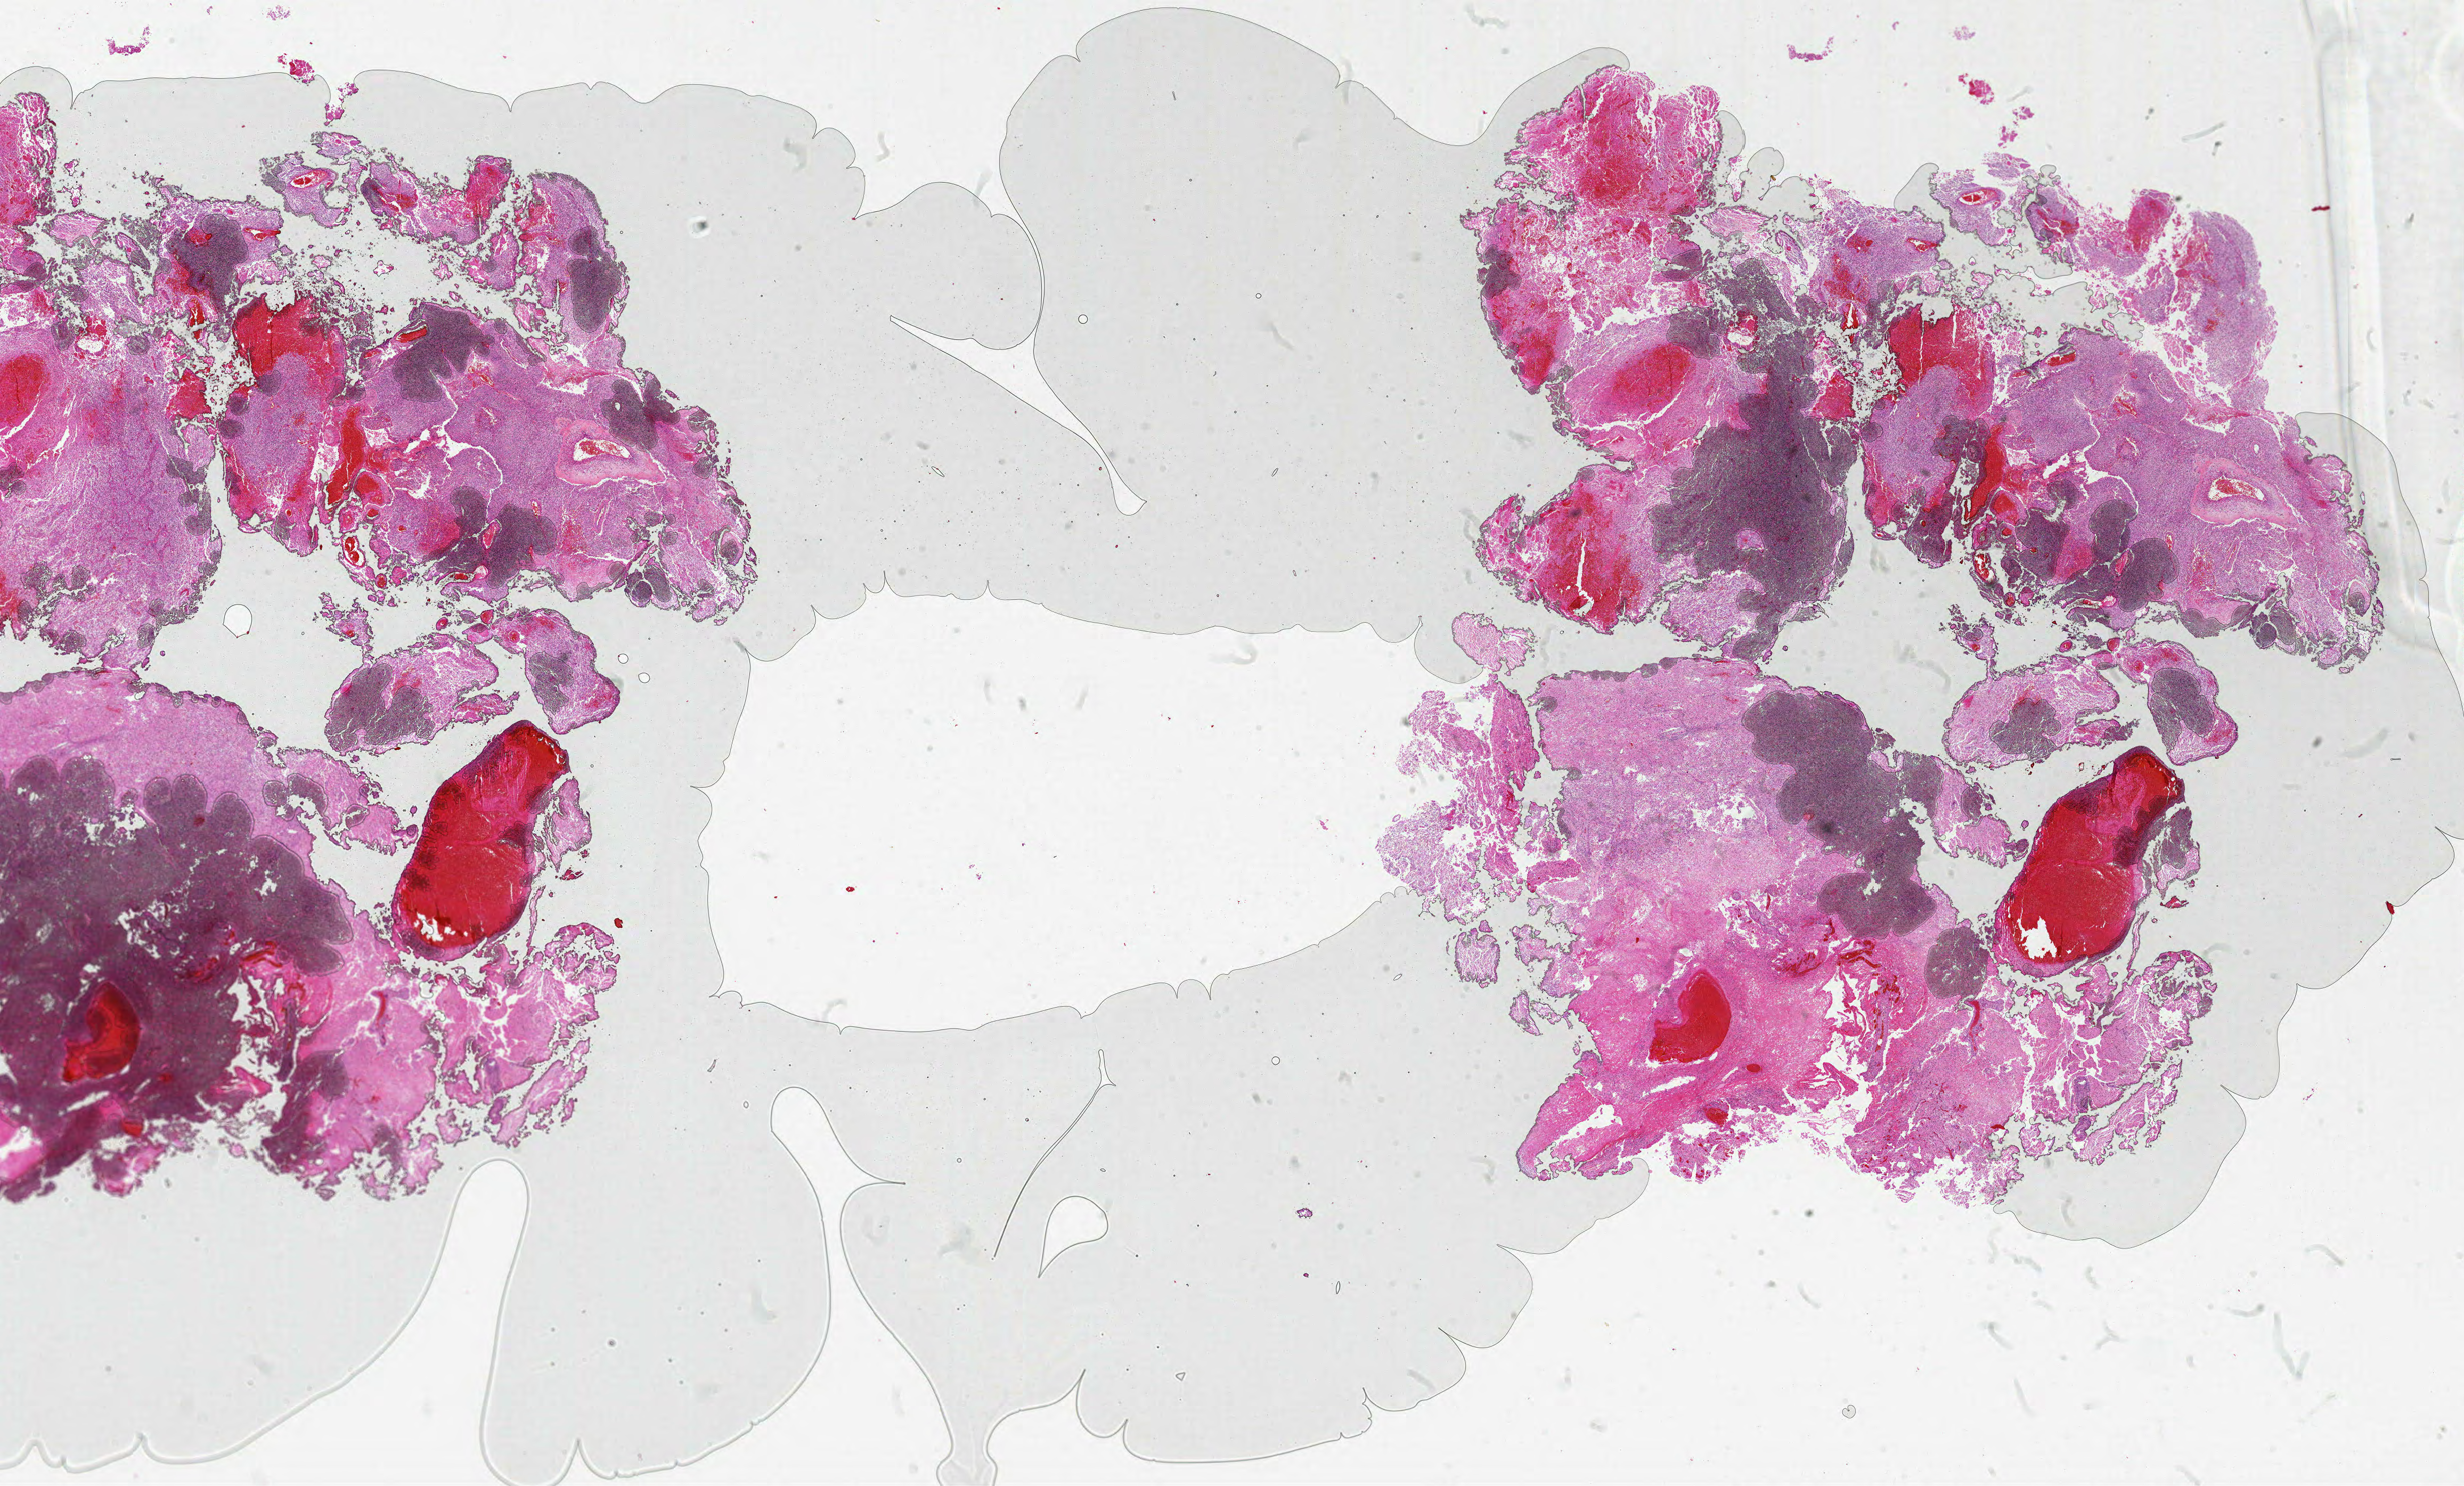
H&E whole-slide image — a low-resolution overview of the entire scanned area, about 37.0 x 22.3 mm. Formalin-fixed paraffin-embedded (FFPE) diagnostic section. Primary tumour sample from the brain. Patient: male, age at initial diagnosis 53 years.
Histologic diagnosis: Glioblastoma.